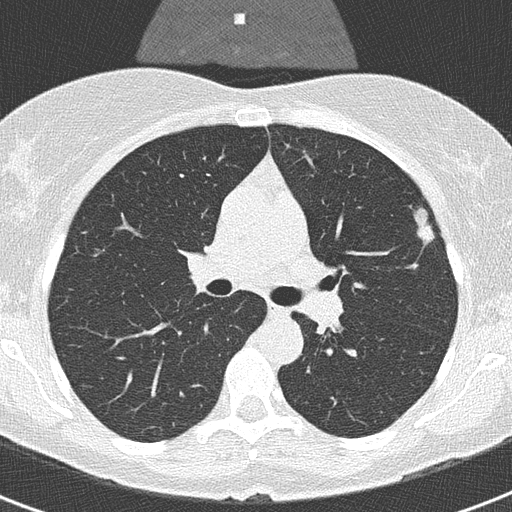
Chest CT (low-dose screening protocol), one axial image. Second screening round (one year after baseline). Lung window (W 1500 / L -600 HU). 2 mm slice thickness. Lung (sharp) reconstruction kernel (B50f). 120 kVp. Slice 114 of 320 in the series. Female, age 56 years at enrolment. Former smoker at enrolment.
- Lesion marked by an expert reader, bounding box <405,201,454,255> (left, top, right, bottom; pixels).
- Reader record for this screening exam (exam-level; its link to the box is not recorded): non-calcified nodule or mass ≥4 mm, left upper lobe, 20 × 9 mm, smooth margins, soft tissue attenuation, pre-existing on the prior screen: yes; interval growth: yes.
- Official screen result: positive, other.